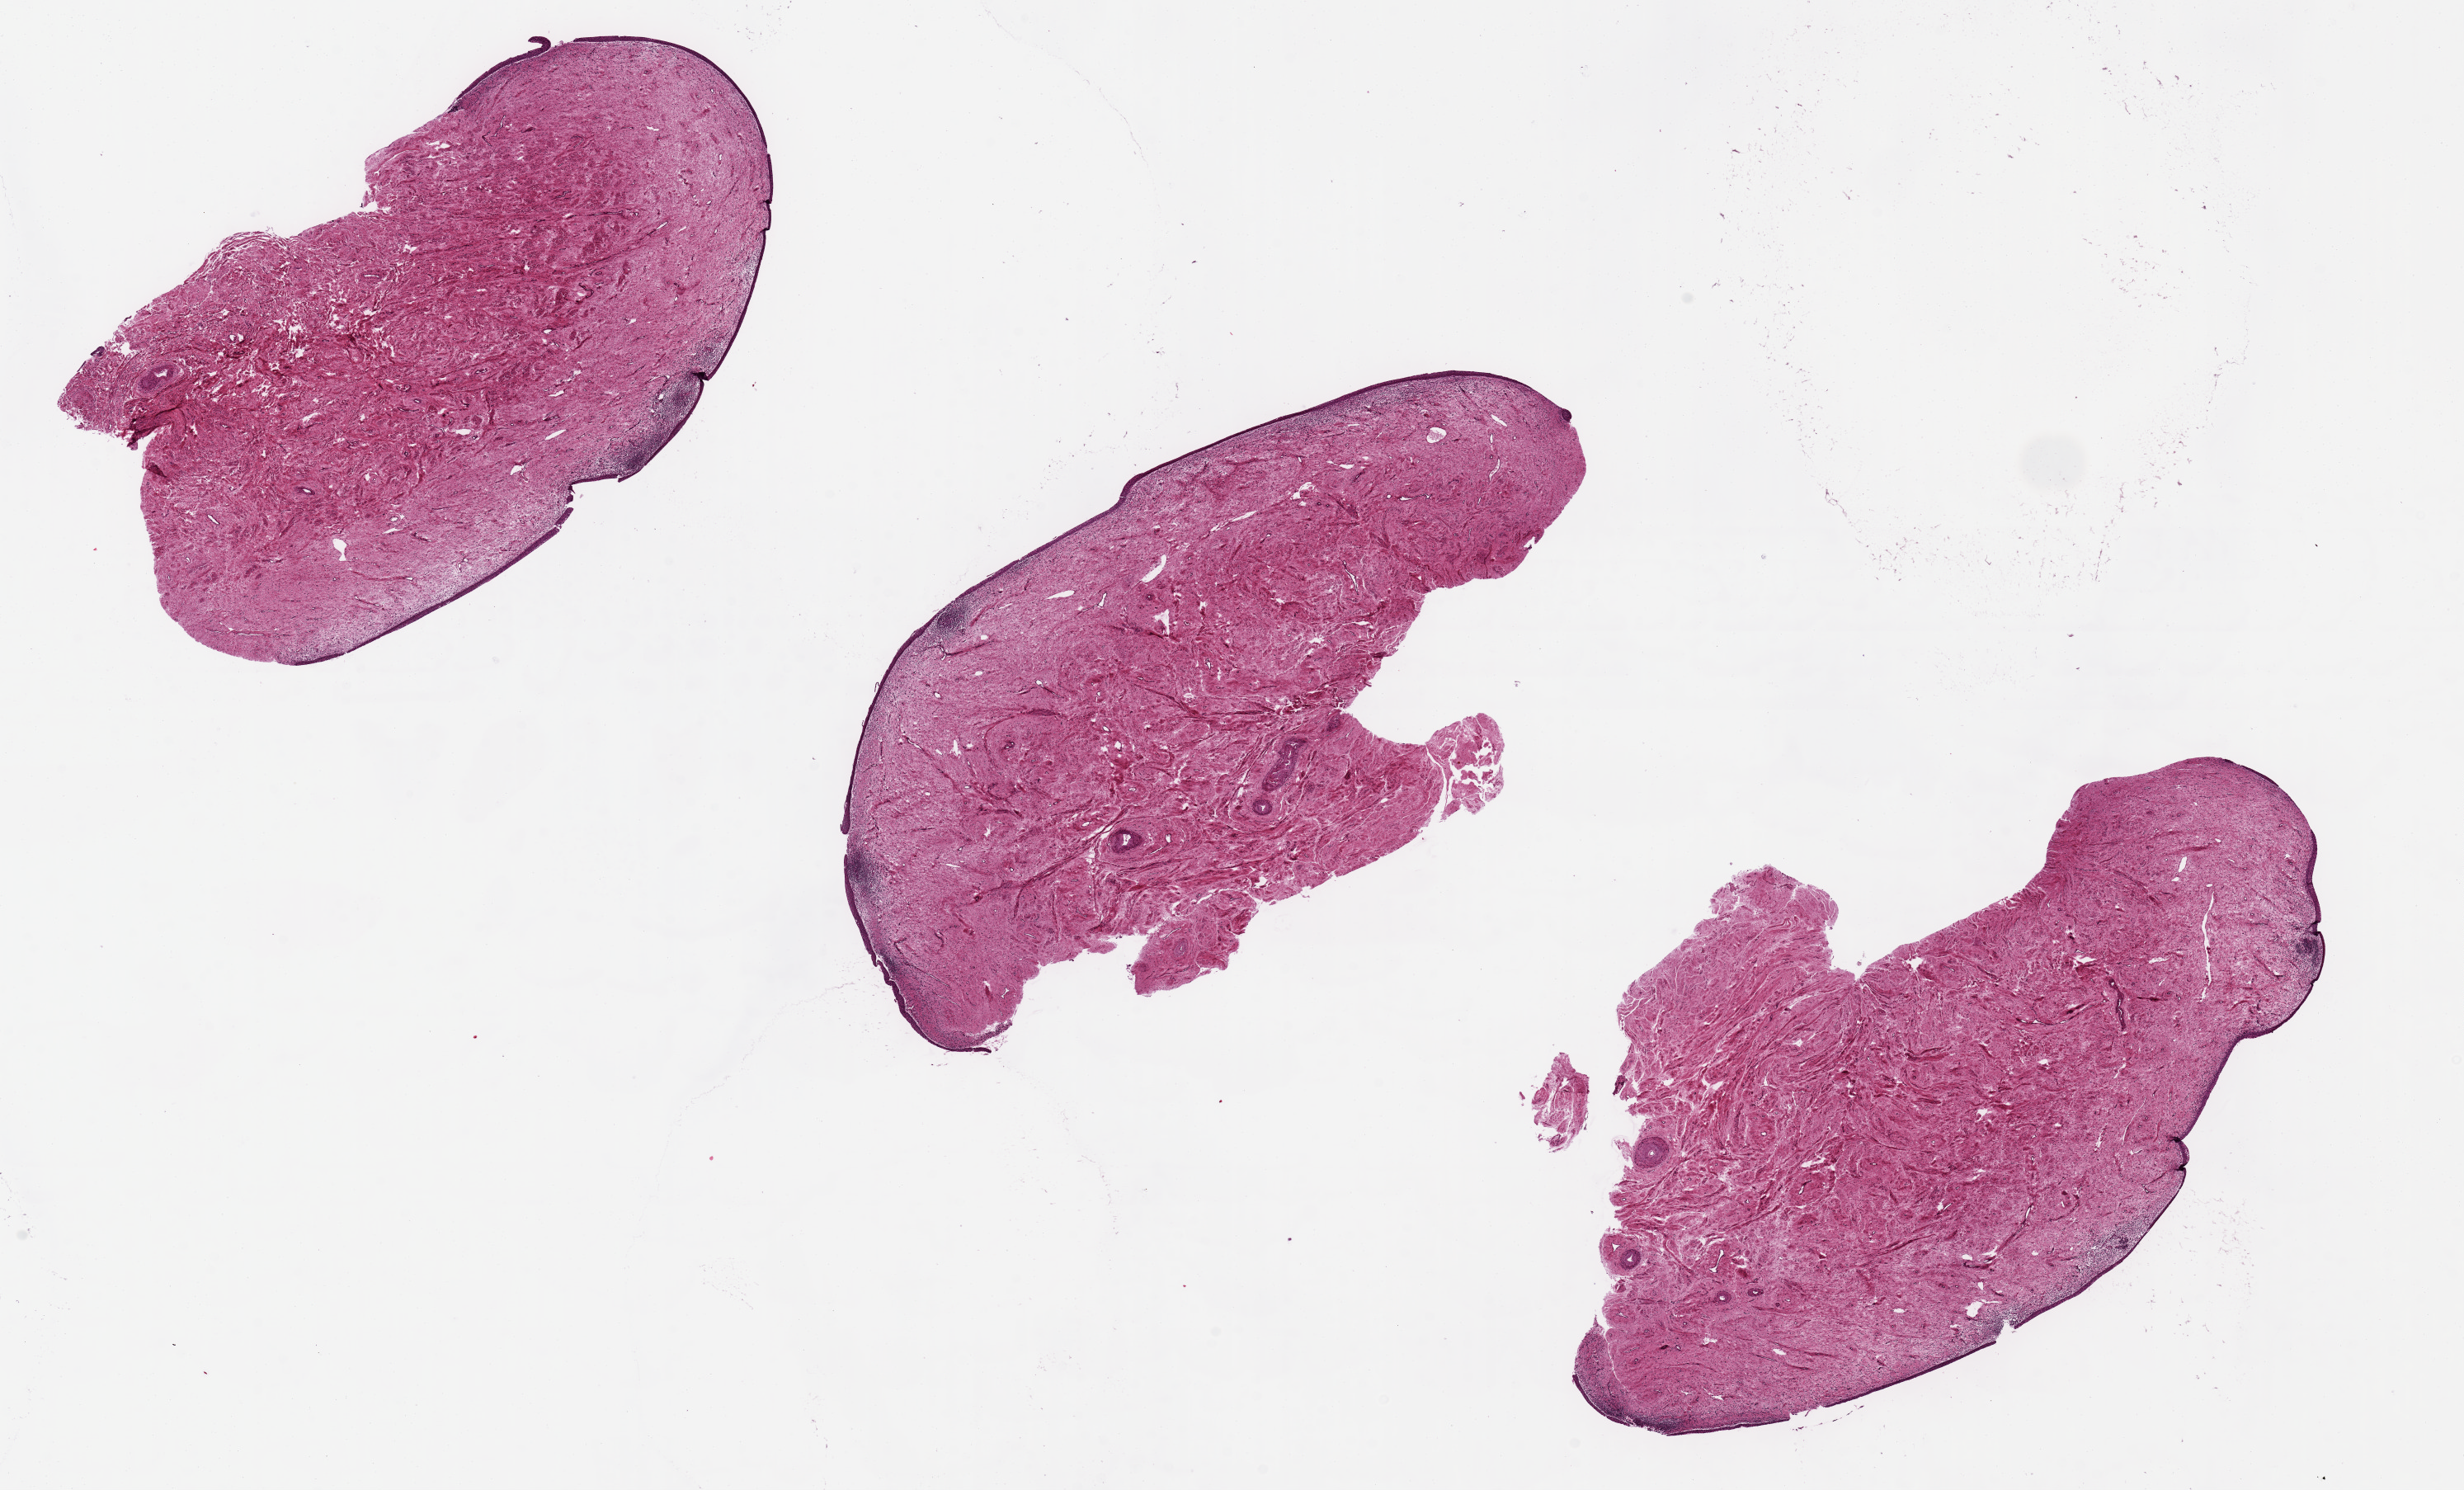
H&E whole-slide image, brightfield — shown as a low-resolution overview of the whole scanned area (about 23.6 x 14.3 mm, slide scanned at 20x); PAXgene-fixed, paraffin-embedded tissue; target tissue: vagina; tissue donor sample.
Review note (as recorded): 3 pieces. Mild chronic inflammation.